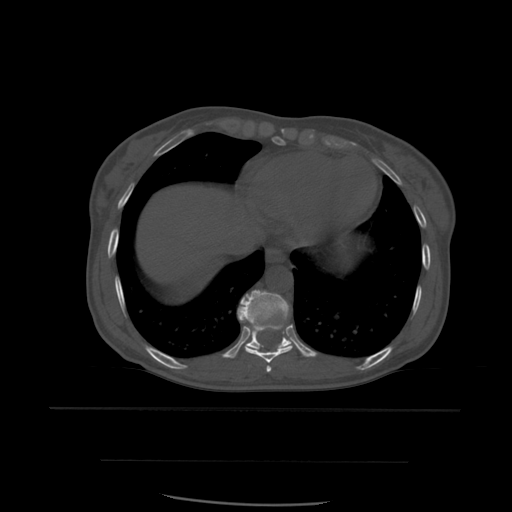
CT including the spine, one axial slice. Slice 328 of 574 in the series (ordered by position). Bone window (W 1800 / L 400 HU). 1.25 mm slice thickness. 512 × 512 image matrix. Patient age 48 years. Case-level facts recorded for this patient, not image findings: primary cancer: lung.
Outlined on this slice (semi-automatically segmented with operator editing):
- T10 vertebra: box from (x=238, y=290) to (x=291, y=349) px
- T8 vertebra: (x=266, y=366)–(x=272, y=373)
- T9 vertebra: (x=240, y=318)–(x=293, y=363)